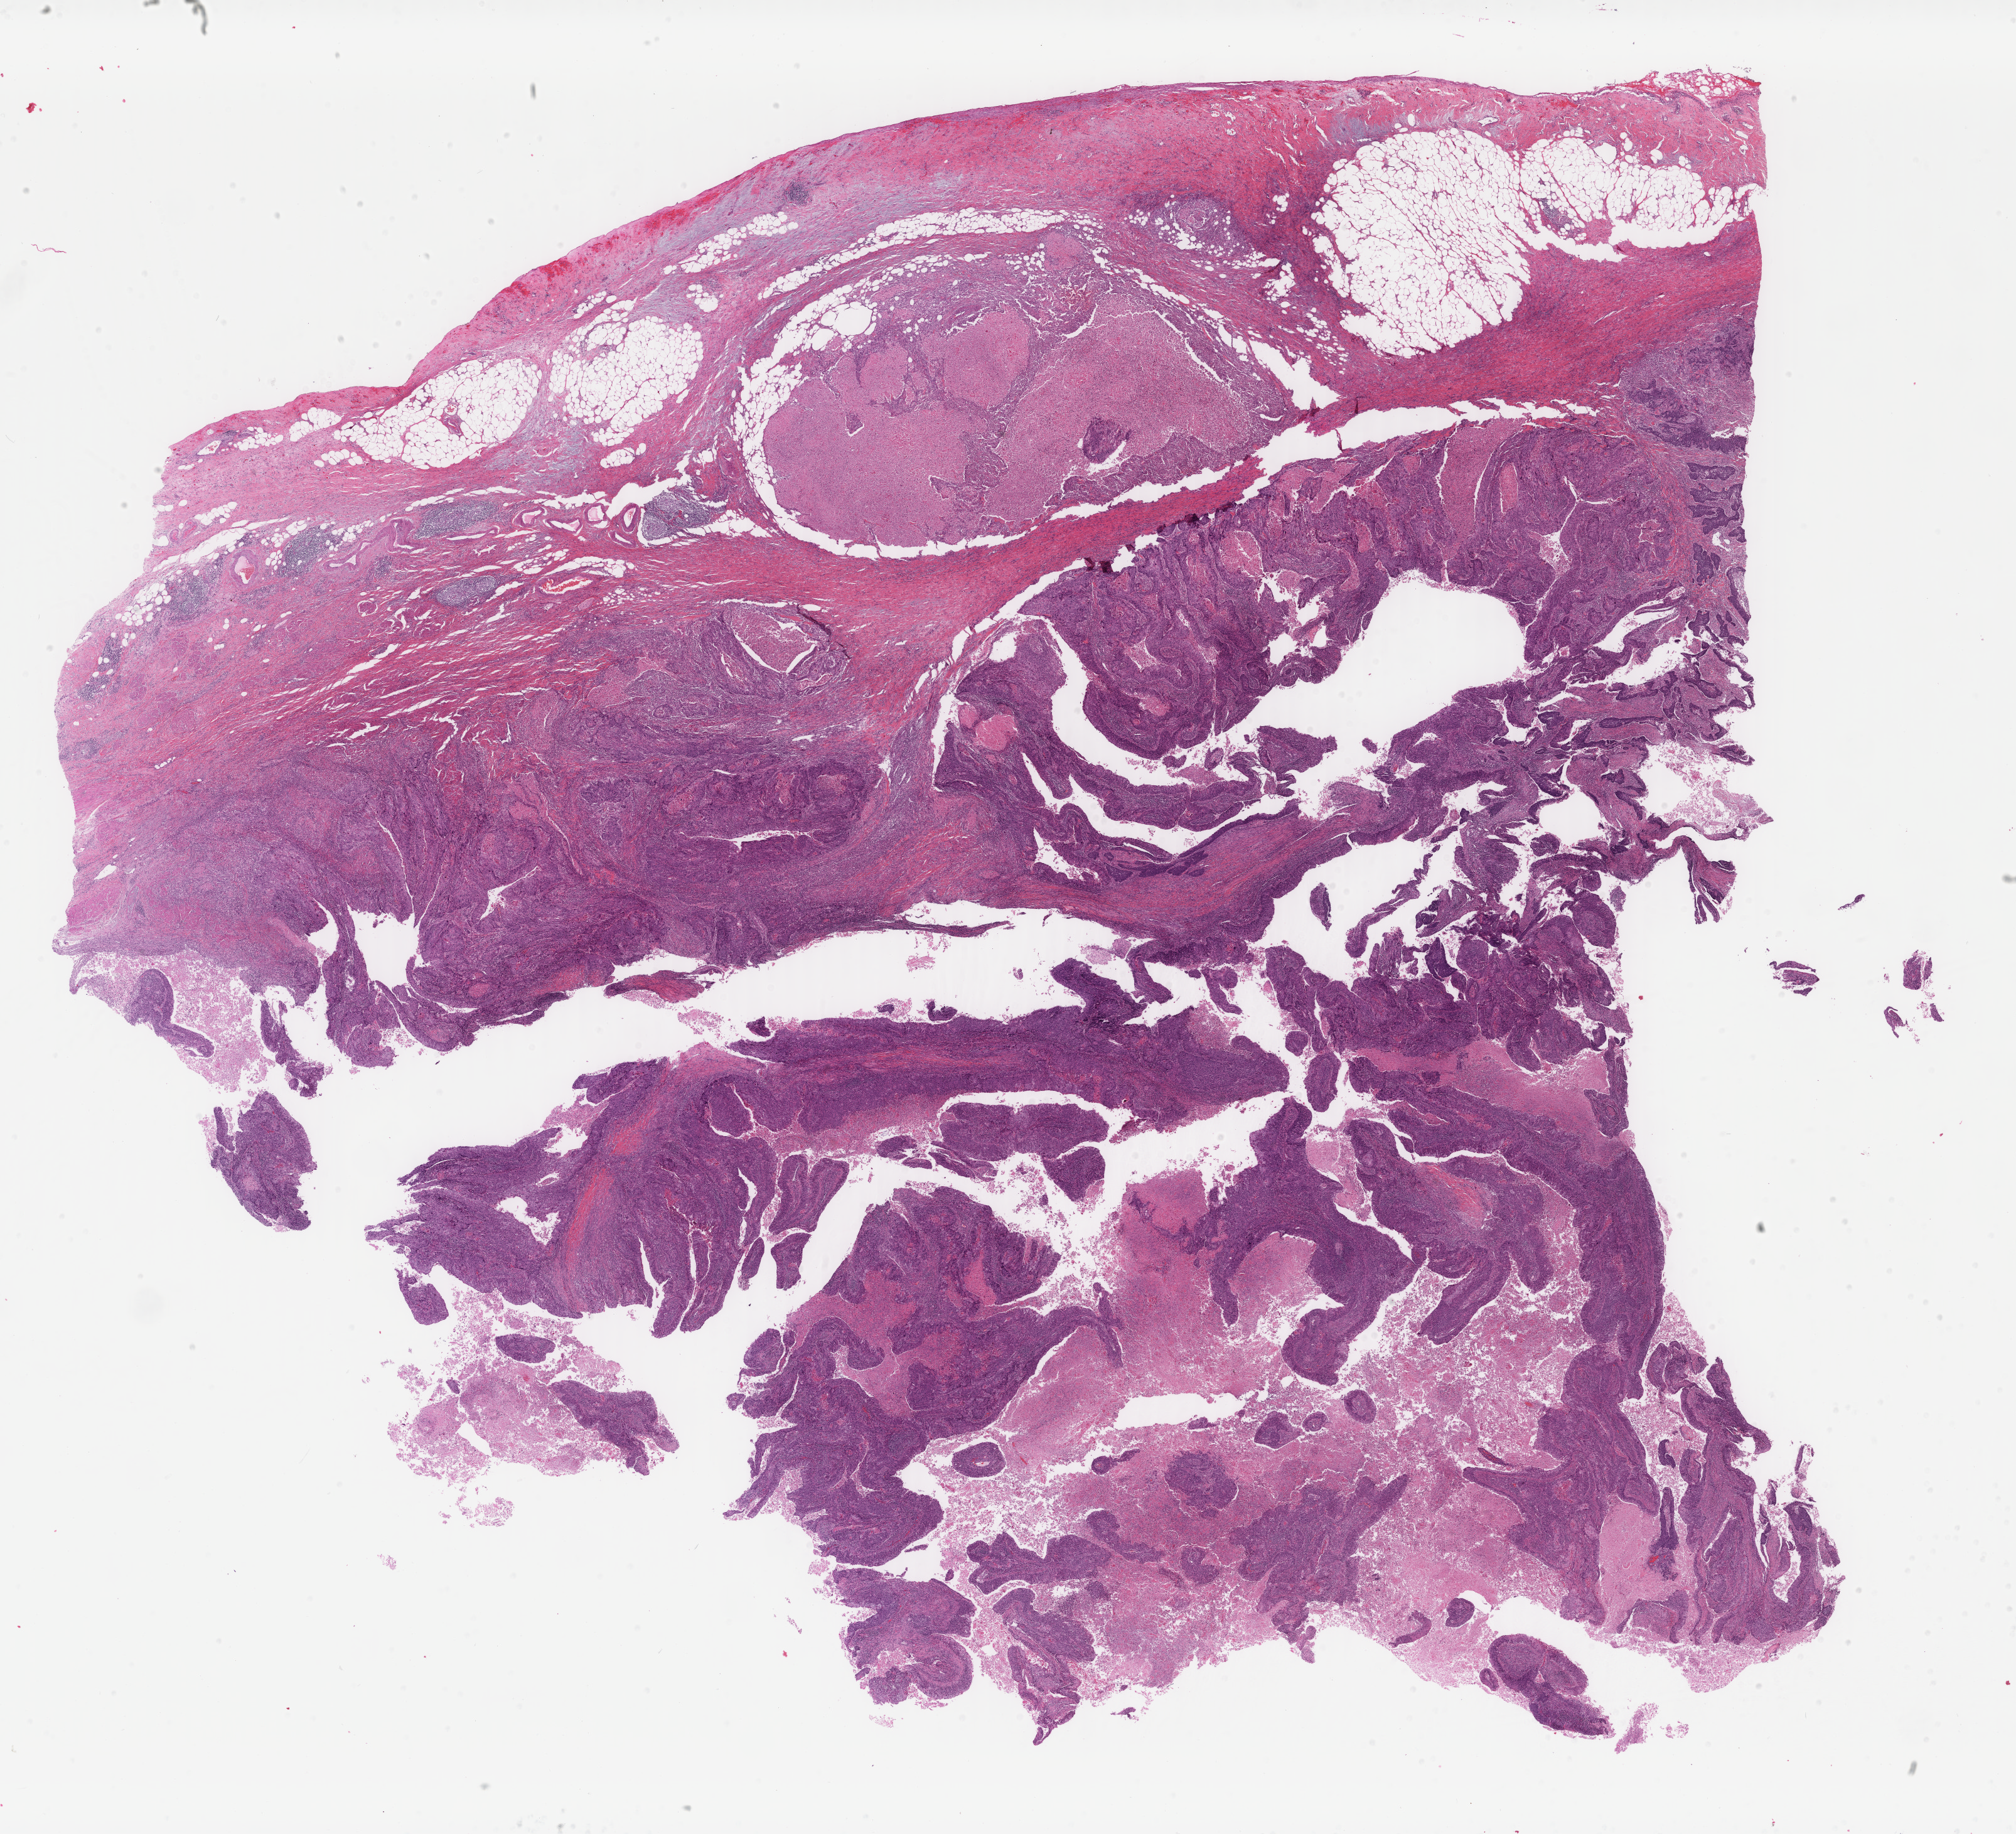
Digitized H&E tissue section (whole slide) — a low-resolution overview of the entire scanned area, about 25.5 x 23.2 mm. Formalin-fixed paraffin-embedded (FFPE) diagnostic section. Sample: primary tumour, bladder. Male, age 85 years at initial diagnosis. Histologic grade: high grade.
• diagnosis: Transitional cell carcinoma
• AJCC pathologic stage: II (6th edition)